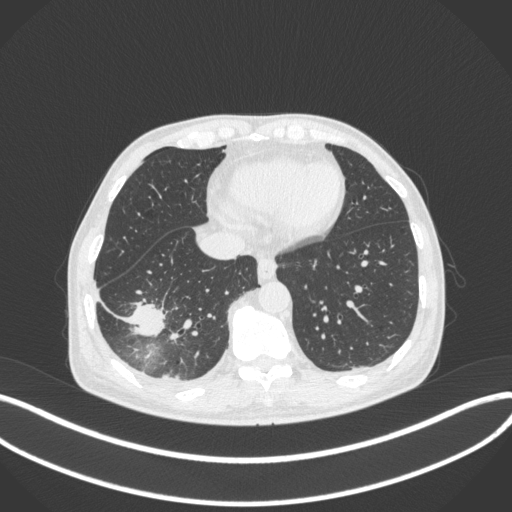
Chest CT, one axial slice; slice 104 of 385 in the series (ordered by position); 120 kVp; lung window (W 1500 / L -600 HU); 1 mm slice thickness; 512 × 512 image matrix, field of view 400 × 400 mm. Male patient, age 64 years. From the clinical record (not read from this slice): clinical TNM (as recorded): T3 N0 M0.
Outlined on this slice (bounding box drawn by a radiologist):
- lung tumour (recorded histology: adenocarcinoma): bounding box [x1, y1, x2, y2] px = [128, 295, 168, 341]